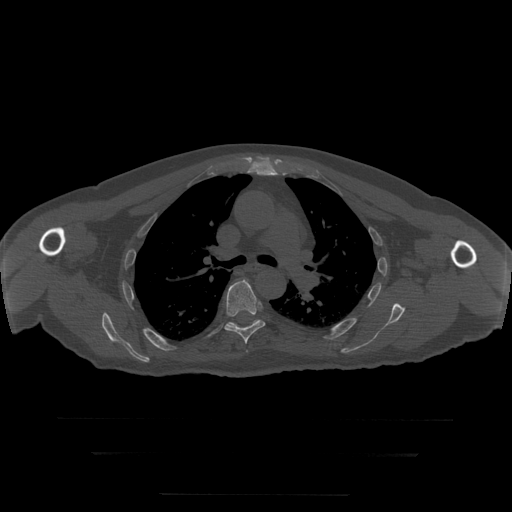
CT including the spine, one axial slice. Position 206 of 397 along the scan axis. Bone window (W 1800 / L 400 HU). 512 × 512 image matrix, field of view 510 × 510 mm. Patient age 73 years. Case-level facts recorded for this patient, not image findings: primary cancer: prostate.
Structures marked on this image (semi-automatically segmented with operator editing):
- T6 vertebra: box from (x=224, y=280) to (x=265, y=344) px
- T7 vertebra: (x=229, y=320)–(x=259, y=326)